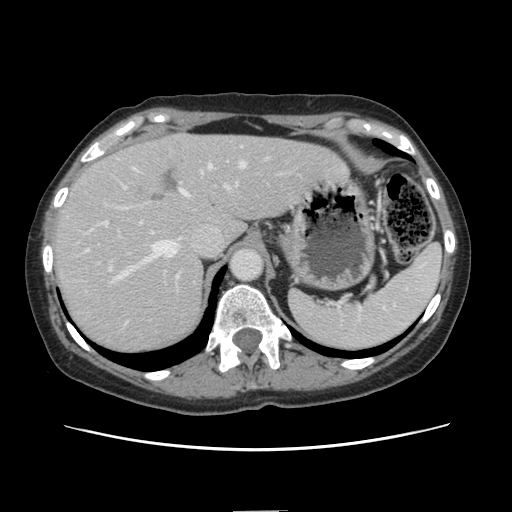
Contrast-enhanced abdominal CT, one axial slice. Position 106 of 141 along the scan axis. 120 kVp. Intravenous contrast given. Soft-tissue window (W 400 / L 40 HU). 512 × 512 image matrix, field of view 350 × 350 mm. Female patient, age 63 years. Case-level facts recorded for this patient, not image findings: diagnosis: colorectal cancer liver metastases, imaged before liver resection; multiple liver metastases: yes; largest metastasis: 3.2 cm; disease in both lobes: yes.
Annotated regions visible in this slice (manually delineated by an expert):
- hepatic veins: box from (x=111, y=162) to (x=245, y=283) px
- liver: (x=53, y=134)–(x=344, y=354)
- planned liver remnant (the part of the liver to remain after resection): (x=187, y=135)–(x=345, y=241)
- portal vein (with intrahepatic branches): (x=103, y=172)–(x=237, y=277)